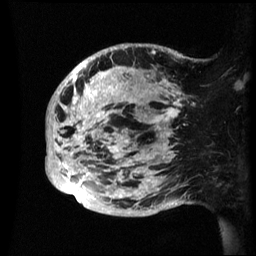
Breast MRI (dynamic contrast-enhanced), one sagittal slice; slice 17 of 60 in the series (ordered by position); dynamic contrast-enhanced series, image 2 of 3 at this slice position (ordered by acquisition); 1.5 T; TE 4.2 ms, TR 8.4 ms; 2.4 mm slice thickness; 256 × 256 image matrix. Female patient, age 48 years.
Annotated regions visible in this slice (semi-automatic segmentation, software-assisted and operator-edited):
- analysis volume of interest (the breast-tissue region the enhancement analysis was run in; not a lesion): bounding box <46,44,192,217> (left, top, right, bottom; pixels)
- tumour enhancement mask (voxels above the 70 % enhancement threshold inside the analysis volume of interest): <46,44,181,201>